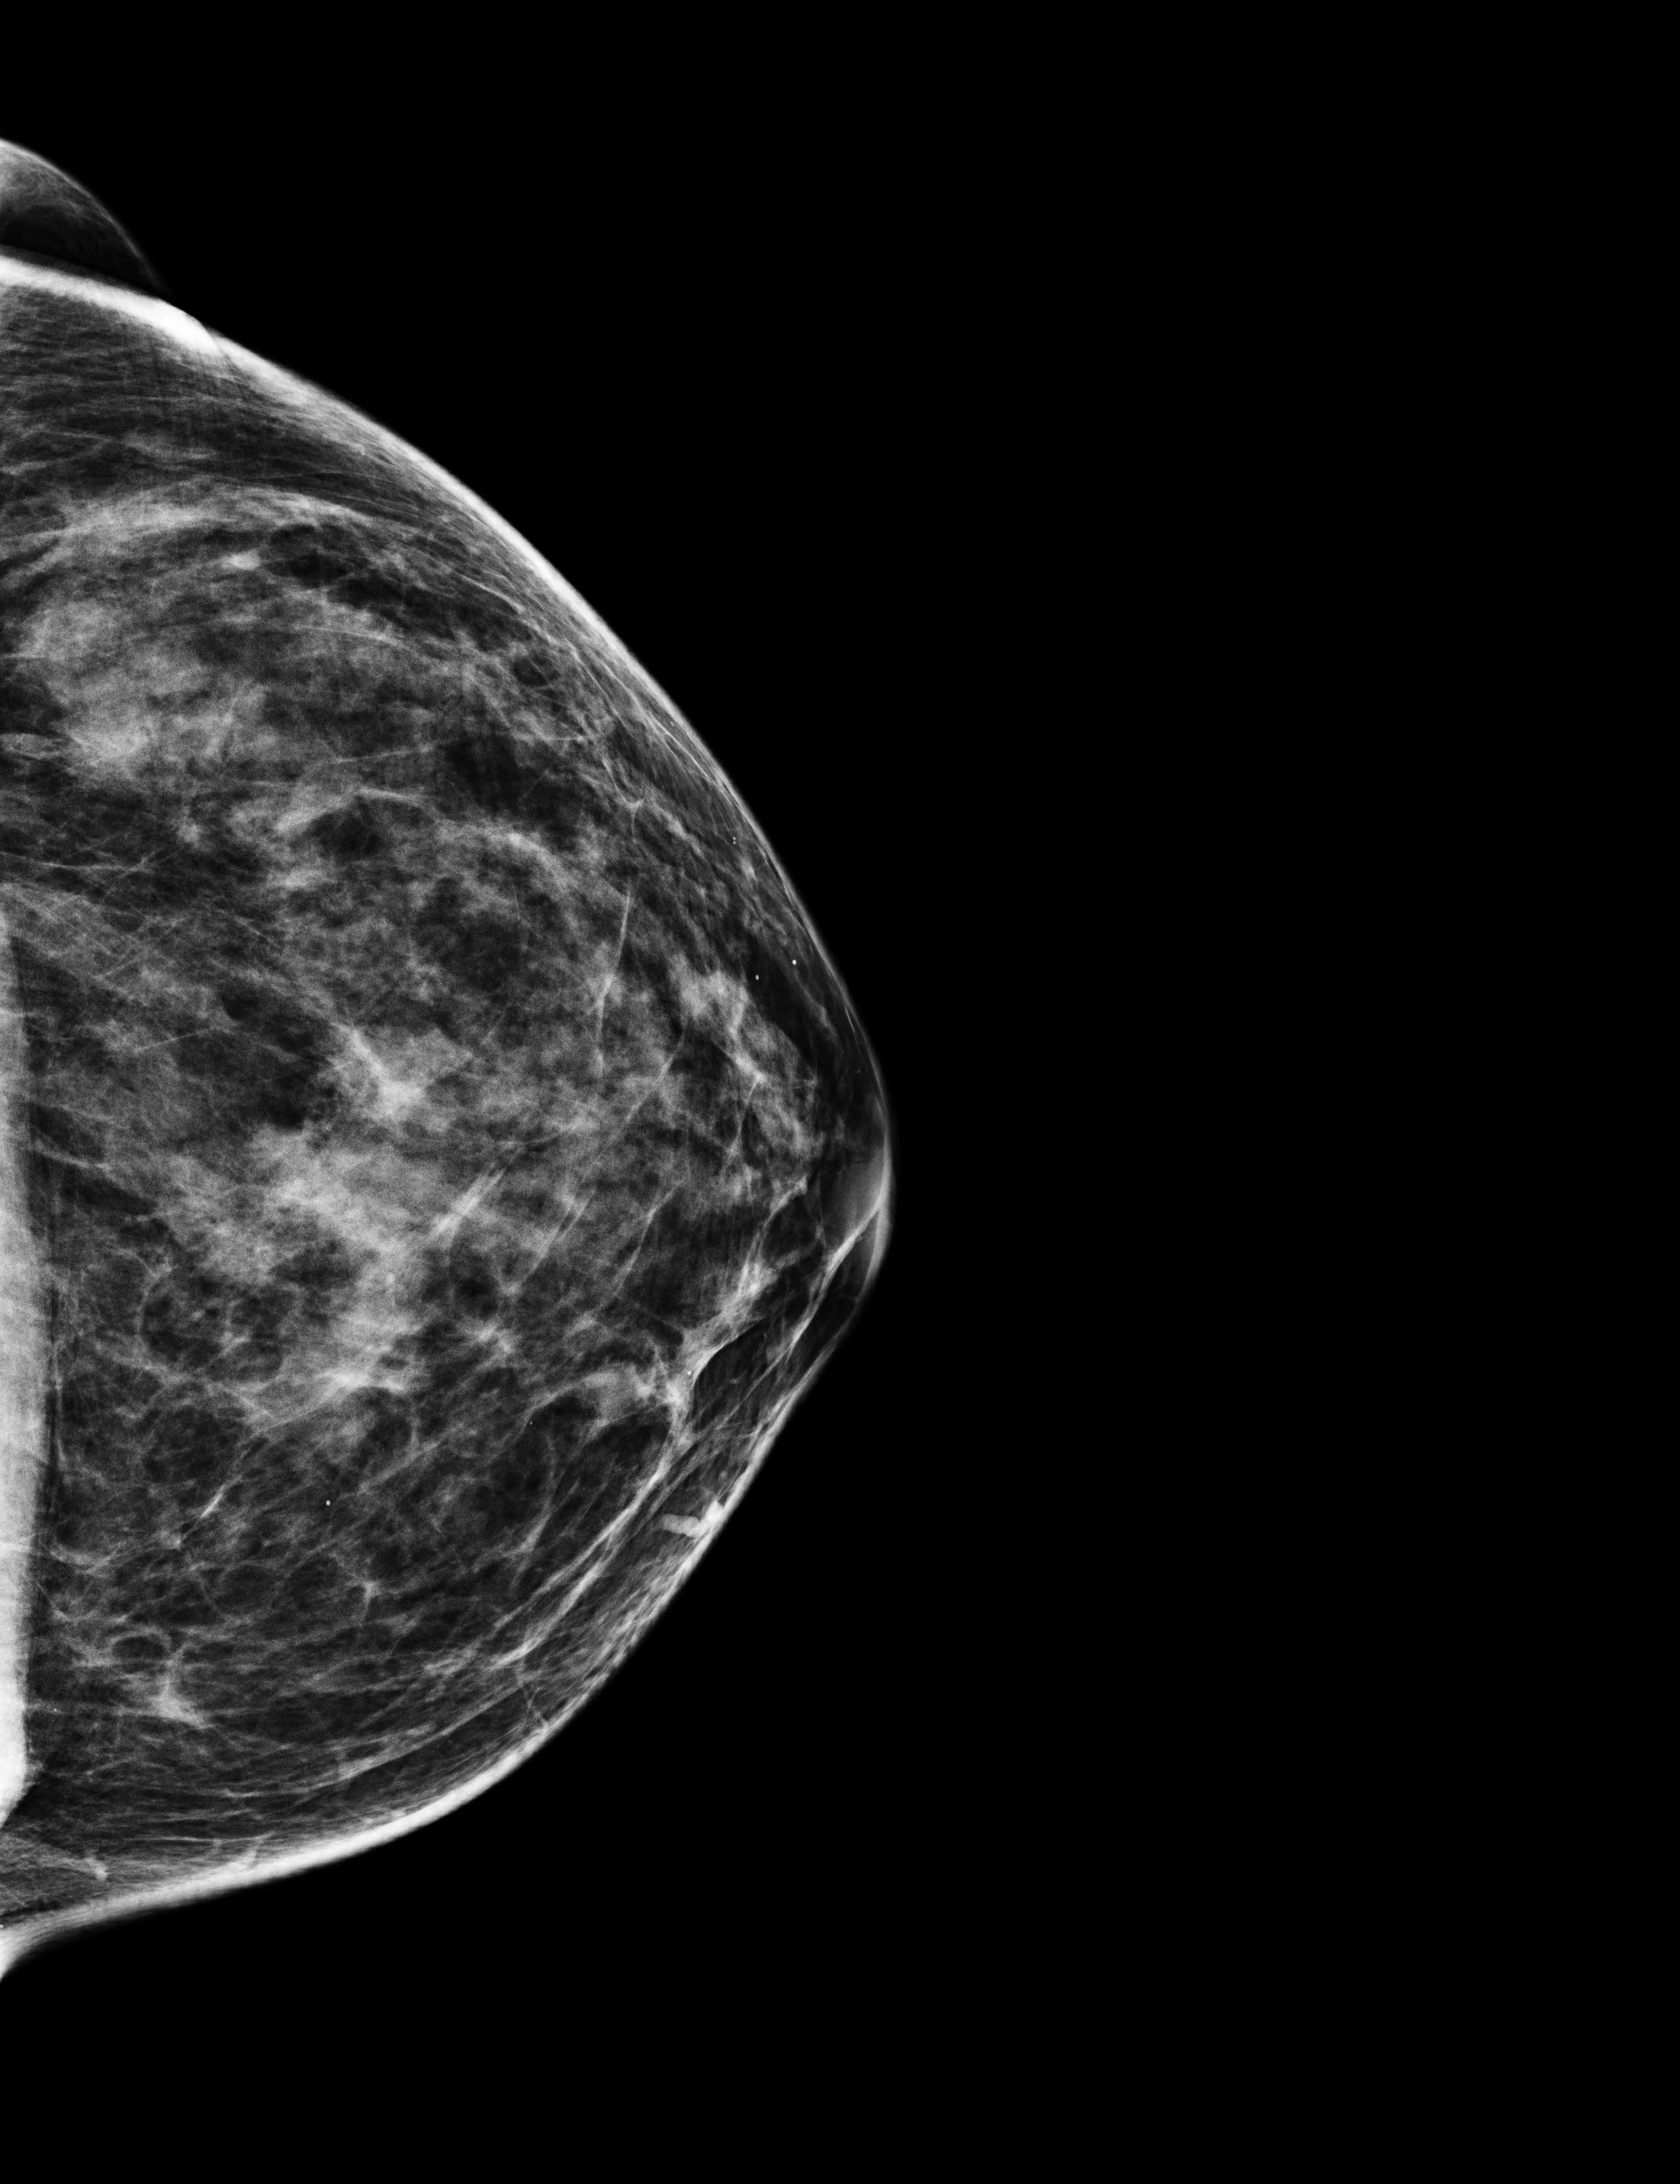
Annual screening mammography examination, compressed breast thickness 49 mm, system: Selenia Dimensions. Patient: female, 44 years.
Image type: full-field digital mammogram. Breast: left. Projection: CC view.